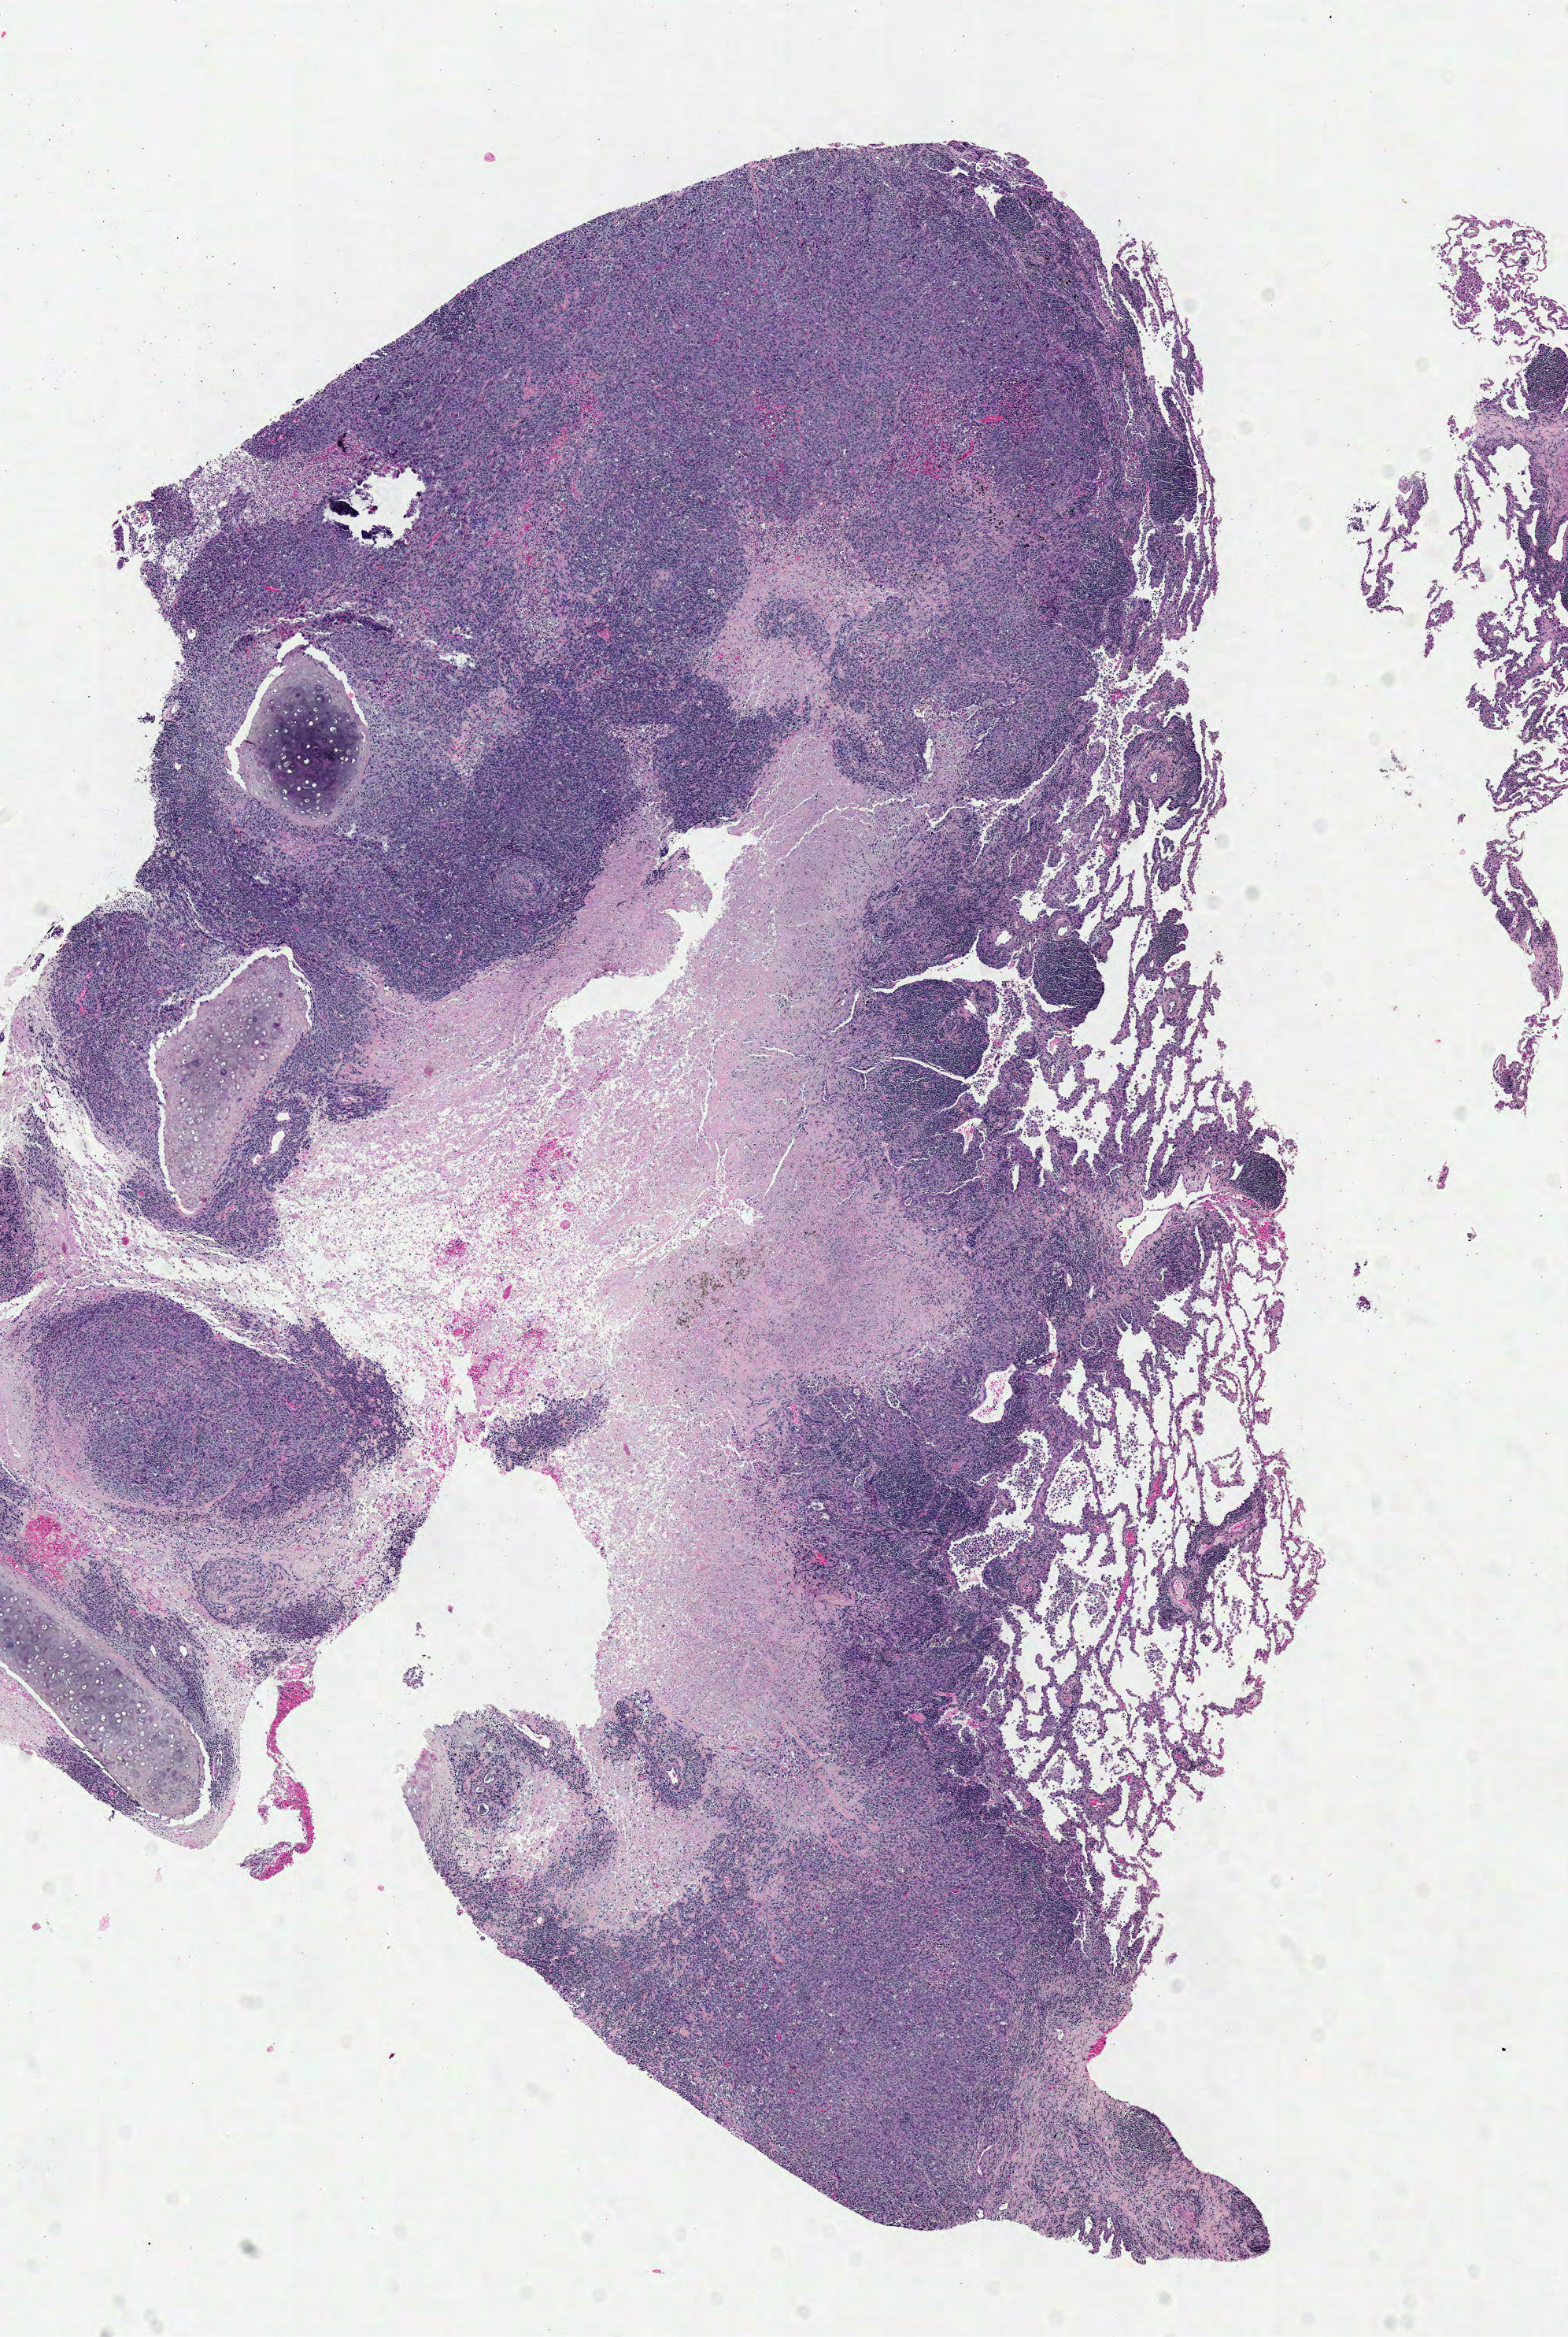
Digitized Hematoxylin and eosin (H&E) stained tissue section (whole slide), shown as a low-resolution overview of the whole scanned area (about 7.8 x 11.7 mm, slide scanned at 40x); formalin-fixed paraffin-embedded (FFPE) diagnostic section; sample: primary tumour, lung. Male patient; age at initial diagnosis 71 years.
Laterality: right. Pathologic diagnosis: Squamous cell carcinoma, NOS (lower lobe, lung). AJCC pathologic stage: IIB (5th edition).